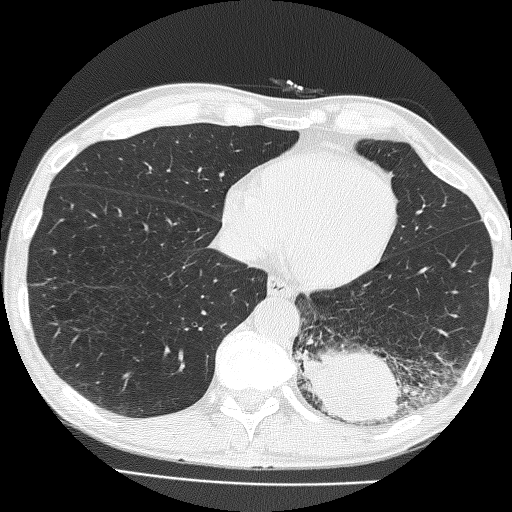
Low-dose screening chest CT, axial slice. Baseline annual screen. Lung window (W 1500 / L -600 HU). 2 mm slice thickness. Lung (sharp) reconstruction kernel (FC51). Slice 108 of 160 in the series. 512 × 512 image matrix, field of view 324 × 324 mm. Male participant, aged 58 years at enrolment. Current smoker at enrolment.
Expert-annotated lung lesion, box from (x=291, y=295) to (x=430, y=435) px. The screening reader recorded 2 non-calcified nodules or masses ≥4 mm on this exam (left lower lobe, left upper lobe); which of them this box marks is not recorded. Official screen result: positive, change unspecified: nodule(s) >= 4 mm or enlarging nodule(s), mass(es), or other non-specific abnormalities suspicious for lung cancer.